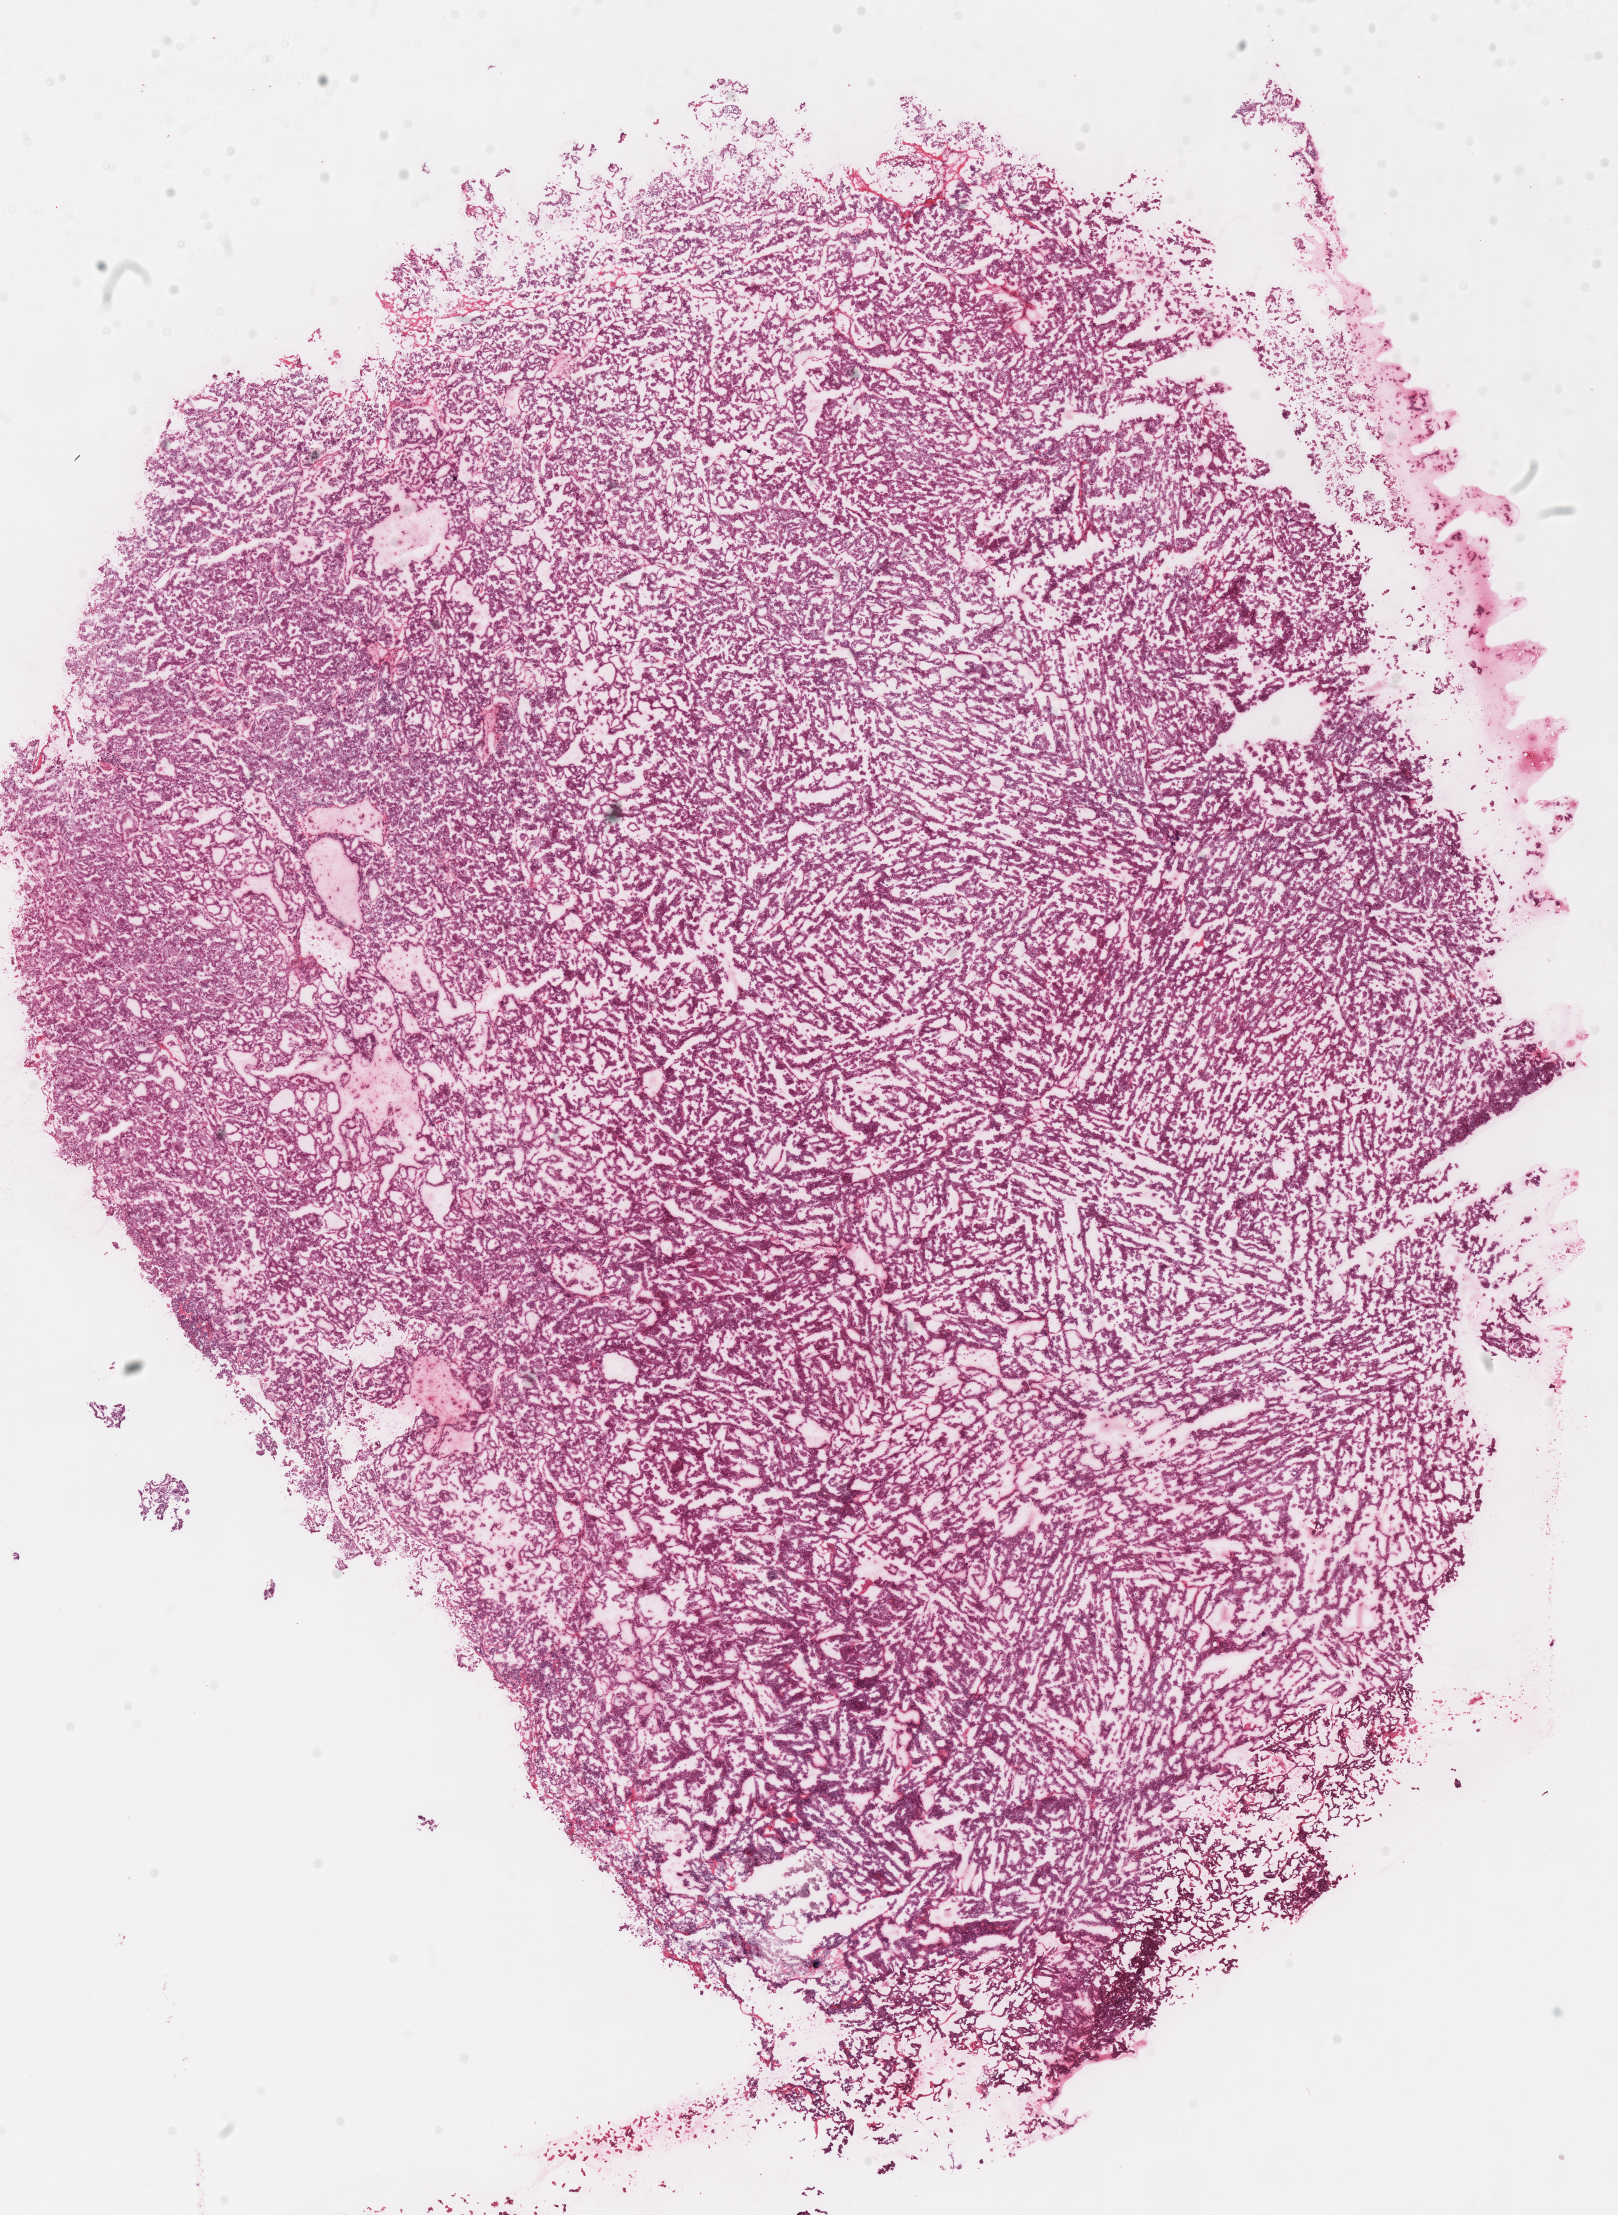
Whole-slide histology image, Hematoxylin and eosin (H&E) stained, a low-resolution overview of the entire scanned area, about 12.7 x 17.4 mm. Frozen section from the top of the tissue portion. Sample: primary tumour, kidney. Female patient; age at initial diagnosis 45 years. Slide review estimates, as recorded: tumour cells 95%, tumour nuclei 95%, normal cells 0%, stromal cells 5%, necrosis 0%.
Diagnosis: Renal cell carcinoma, chromophobe type. AJCC pathologic stage: II (6th edition).